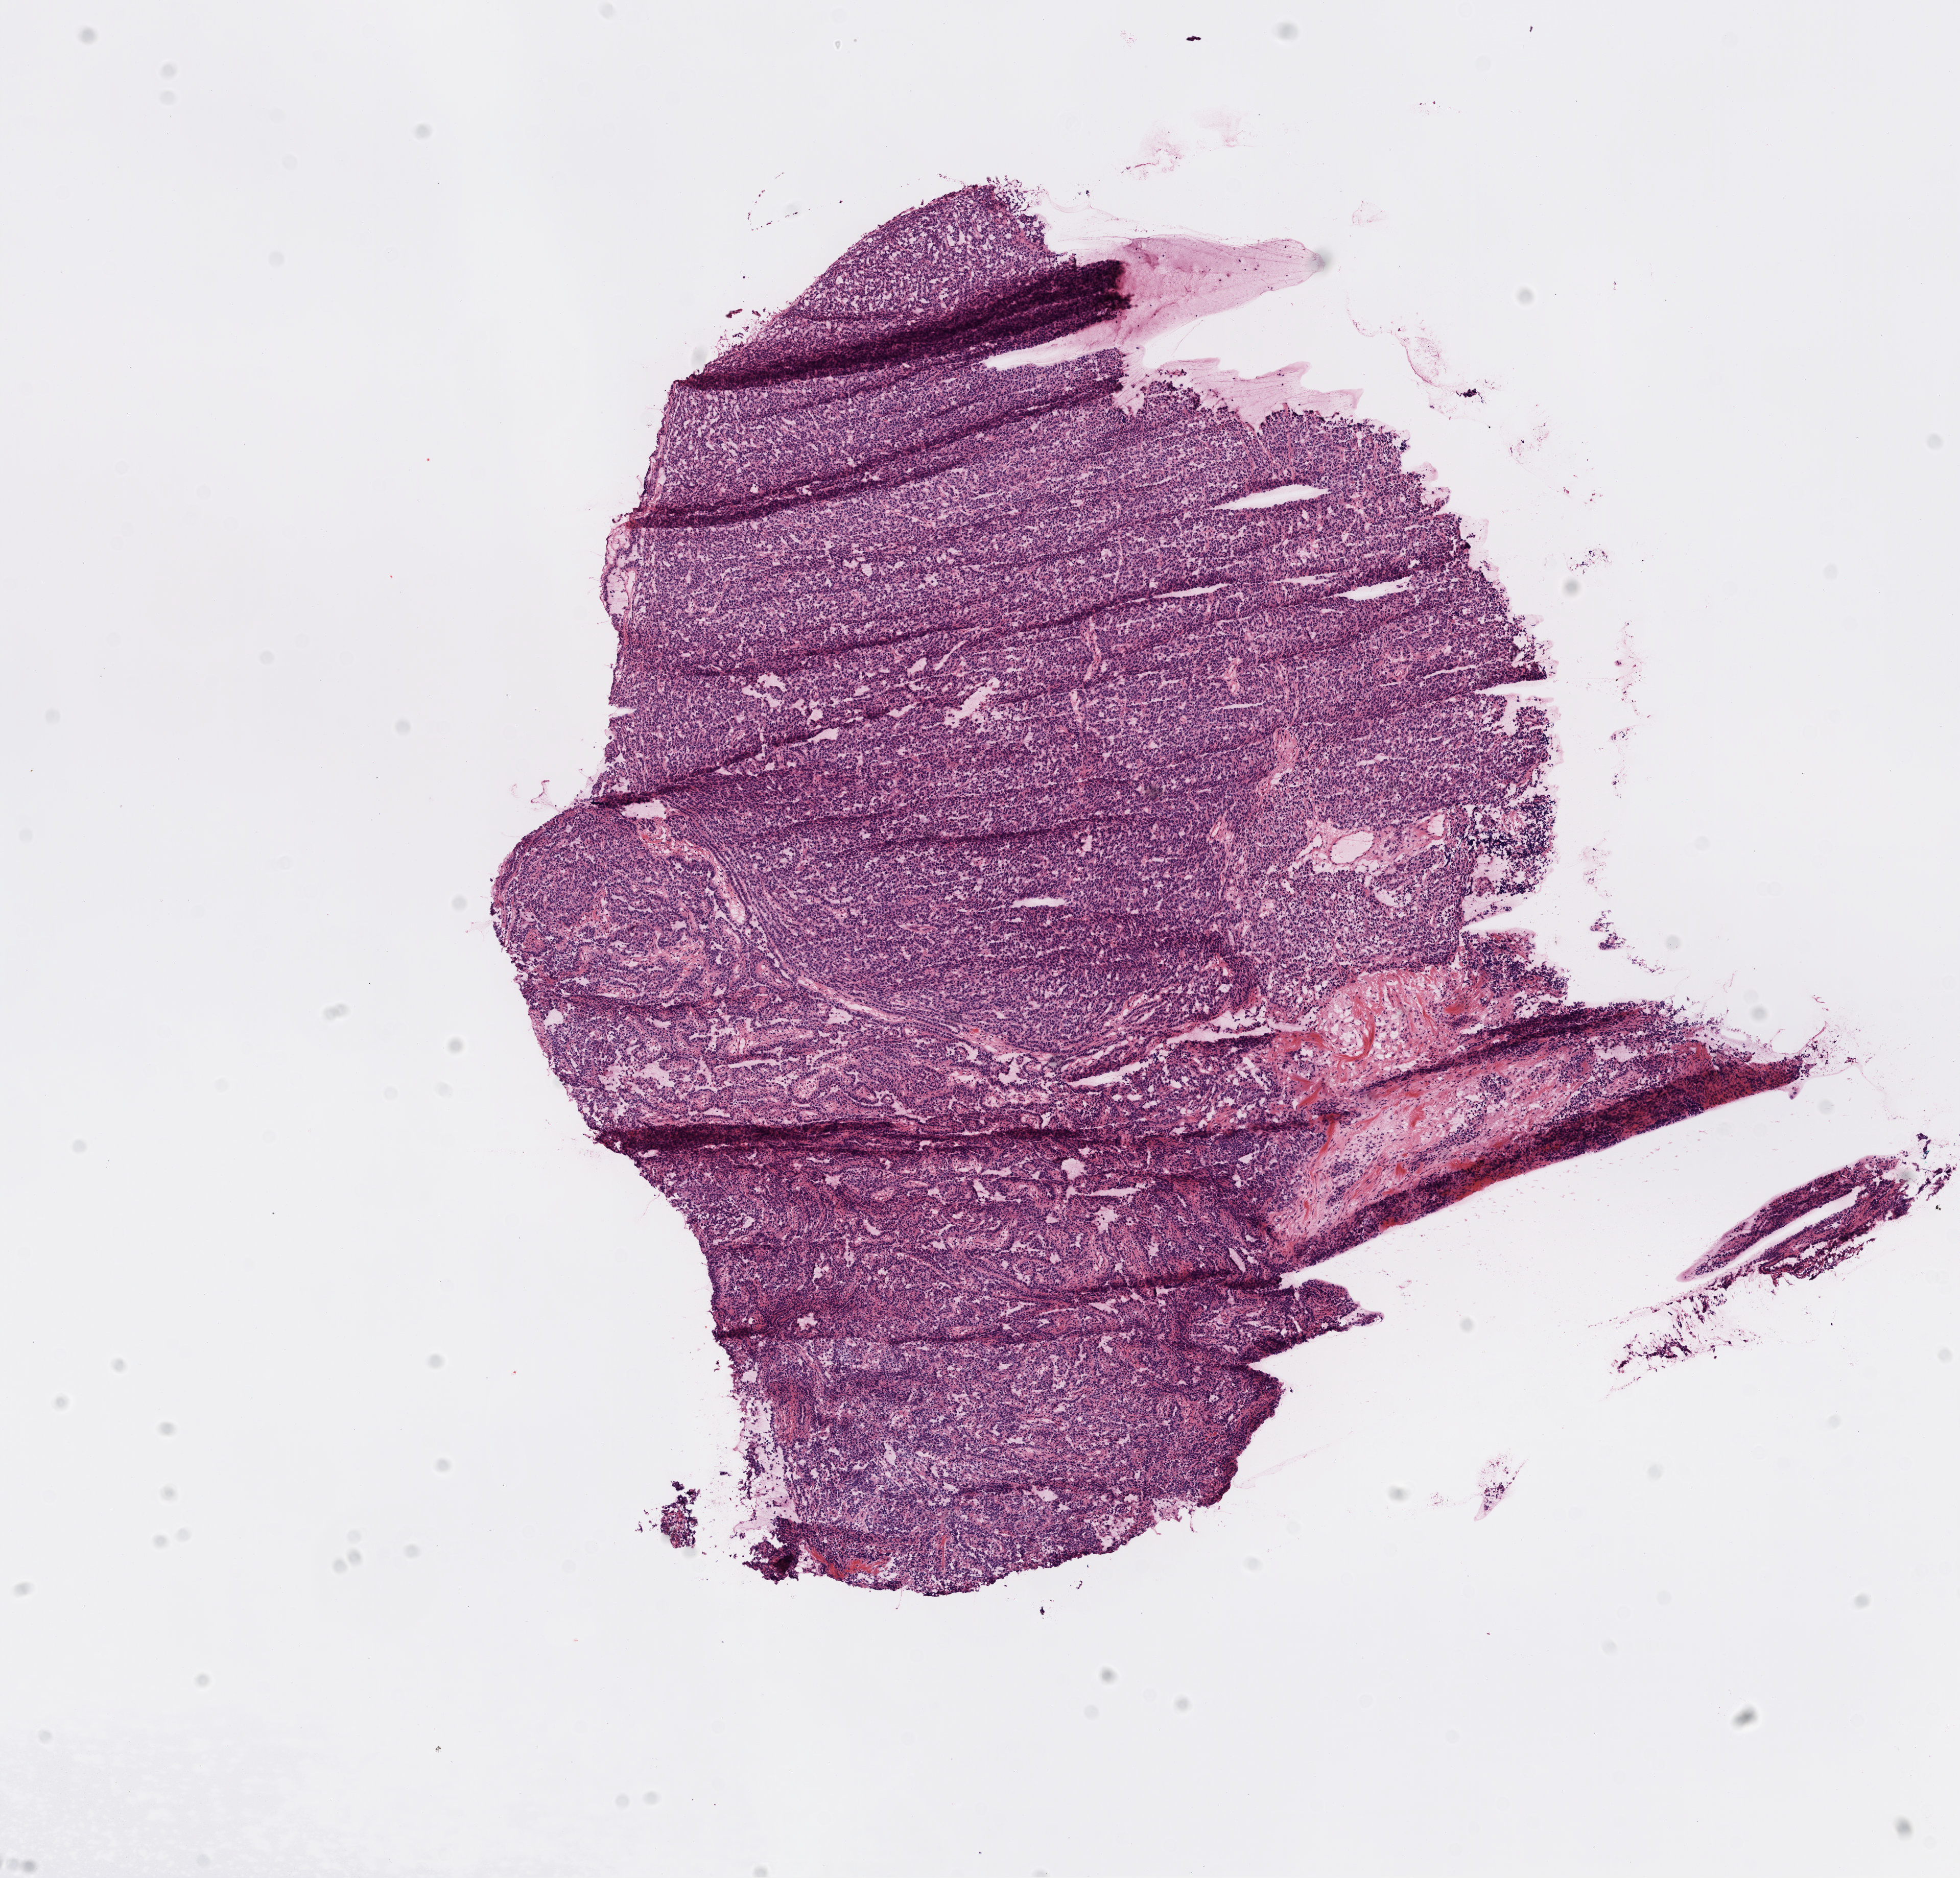
H&E-stained whole-slide image, low-resolution overview of the scanned area, about 7.7 x 7.4 mm (acquisition: 20x scan), frozen section from the top of the tissue portion, sample: primary tumour, ovary. Female patient; age at initial diagnosis 74 years. Histologic grade: G3 (poorly differentiated). Slide review estimates, as recorded: tumour cells 91%, tumour nuclei 95%, normal cells 6%, stromal cells 1%, necrosis 2%.
• diagnosis: Serous cystadenocarcinoma, NOS
• FIGO stage: IIIC